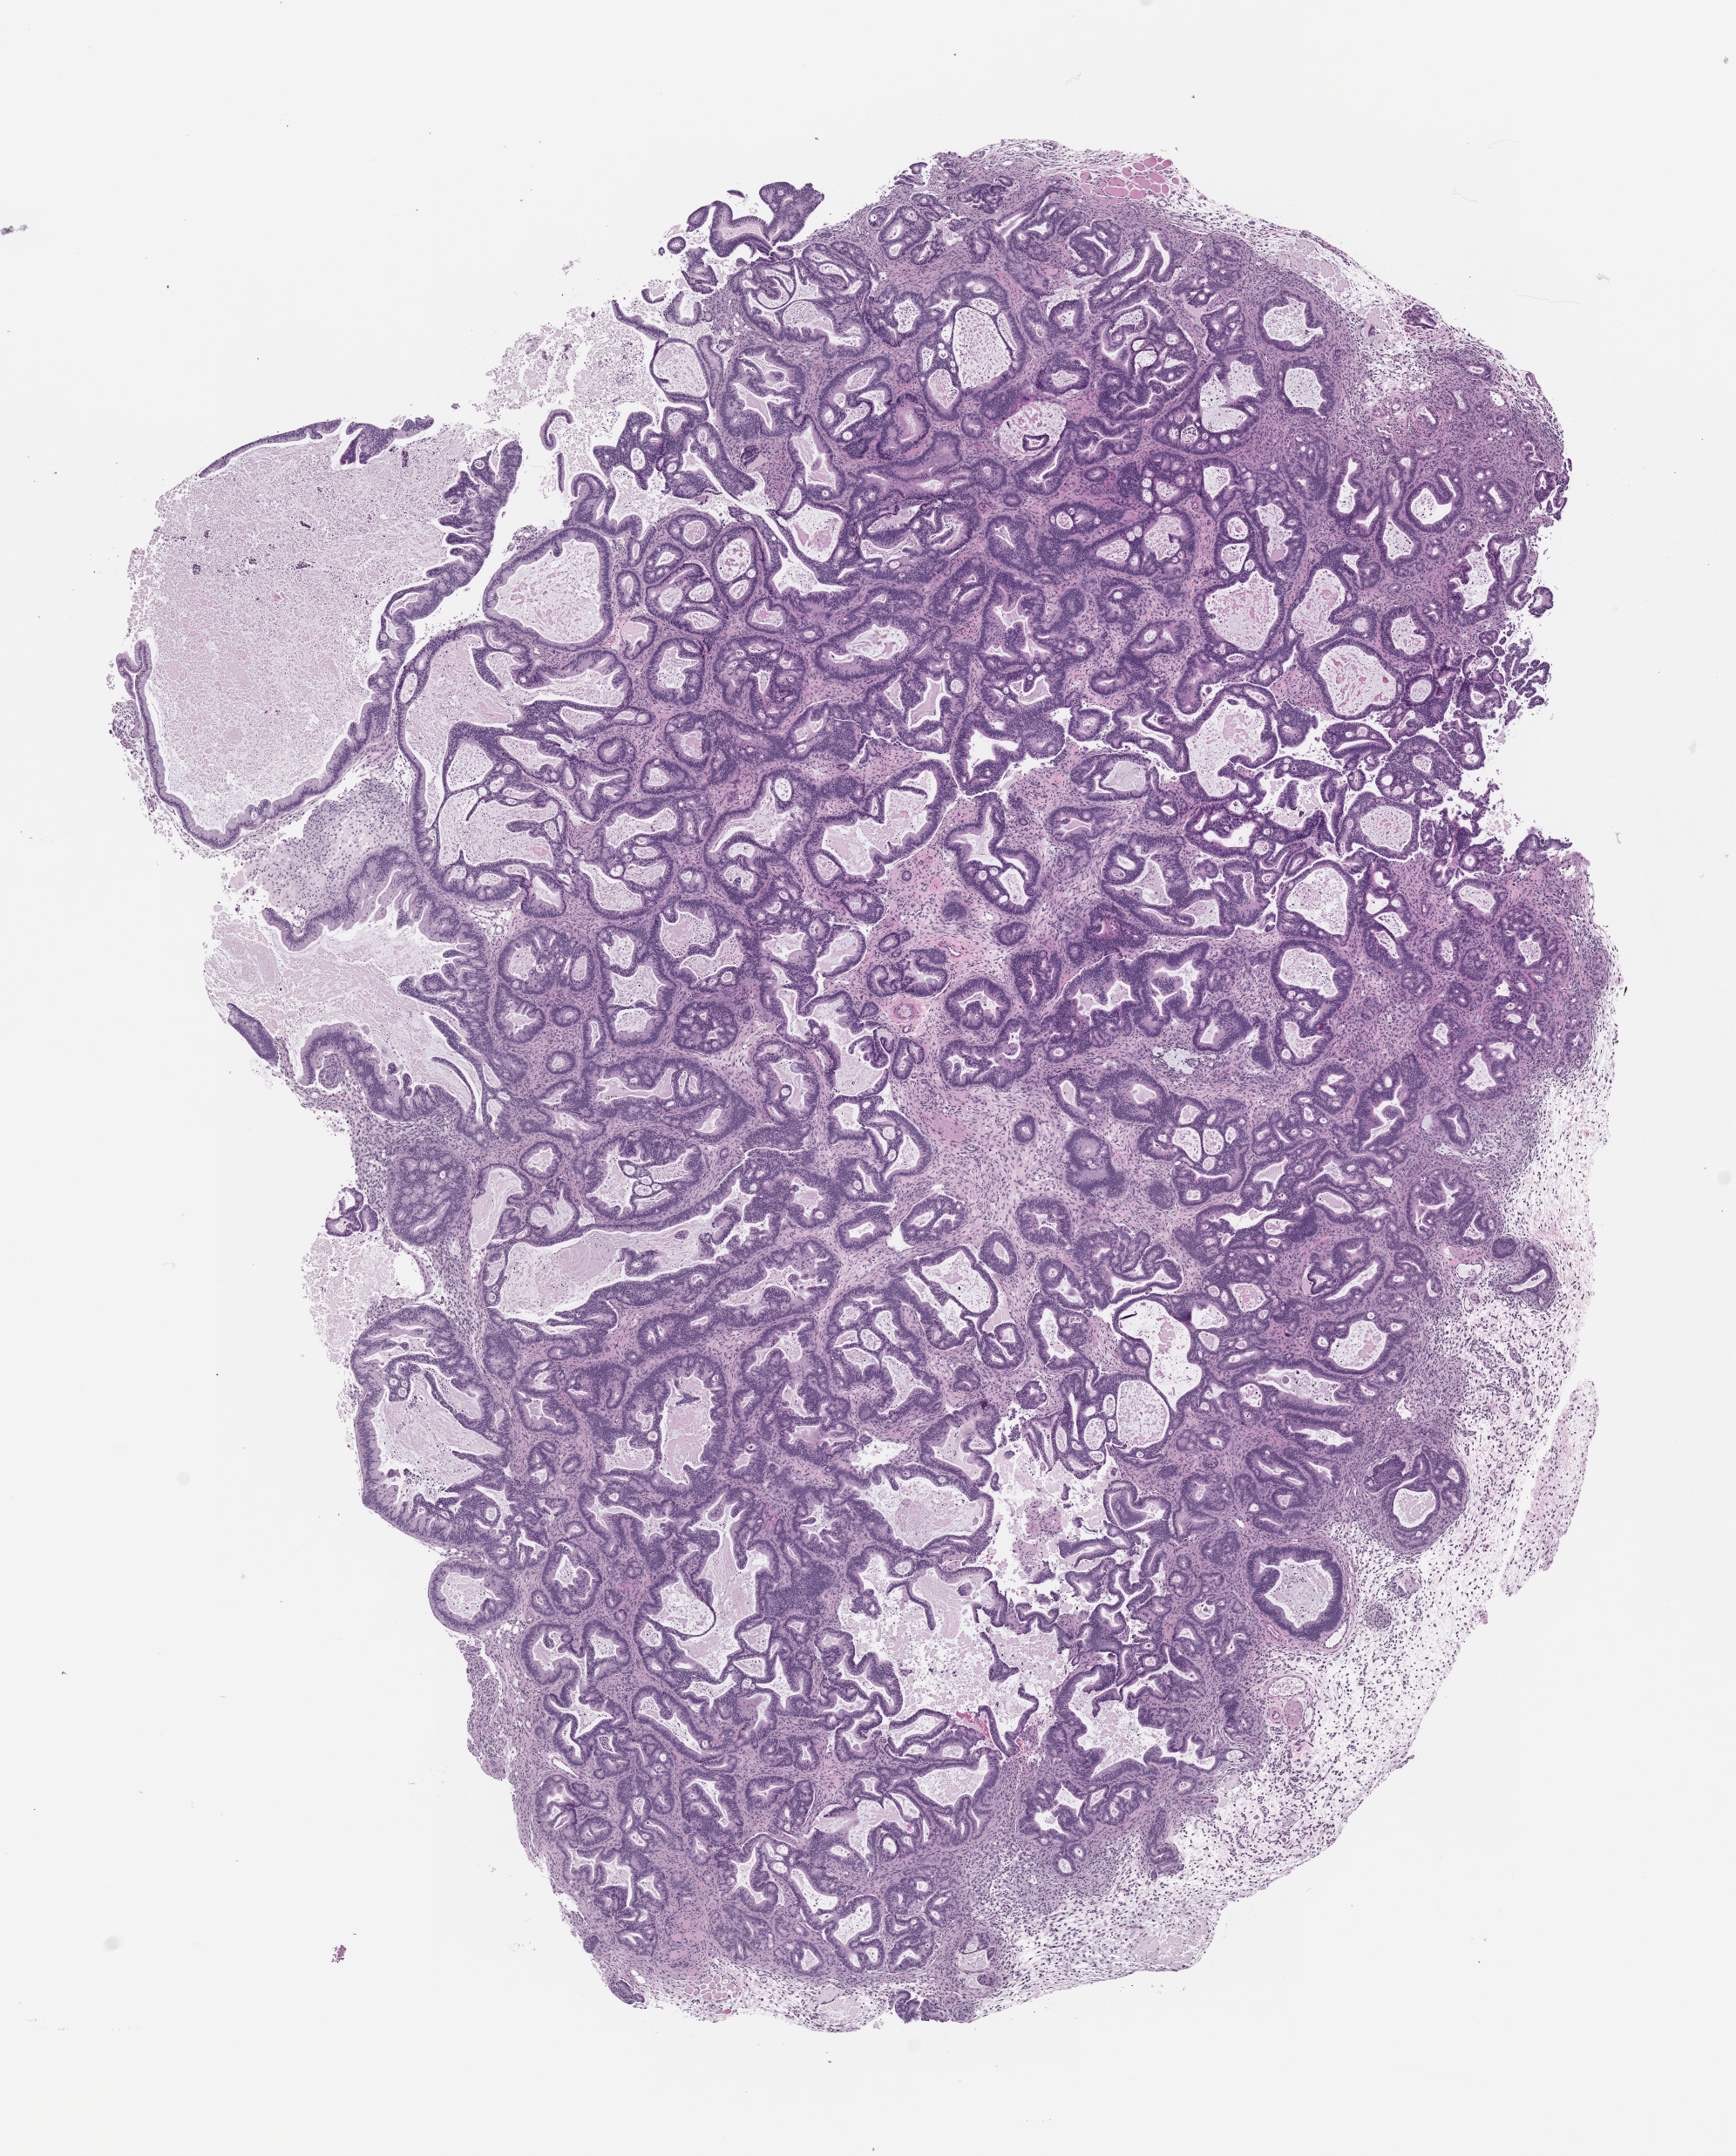
H&E whole-slide image of a patient-derived xenograft (PDX) tumor grown in a mouse, passage 2 — whole scanned area (about 8.0 x 9.9 mm) shown as a low-resolution overview; FFPE section; tumor site category: pancreas.
Originating patient diagnosis: Pancreatic Adenocarcinoma.